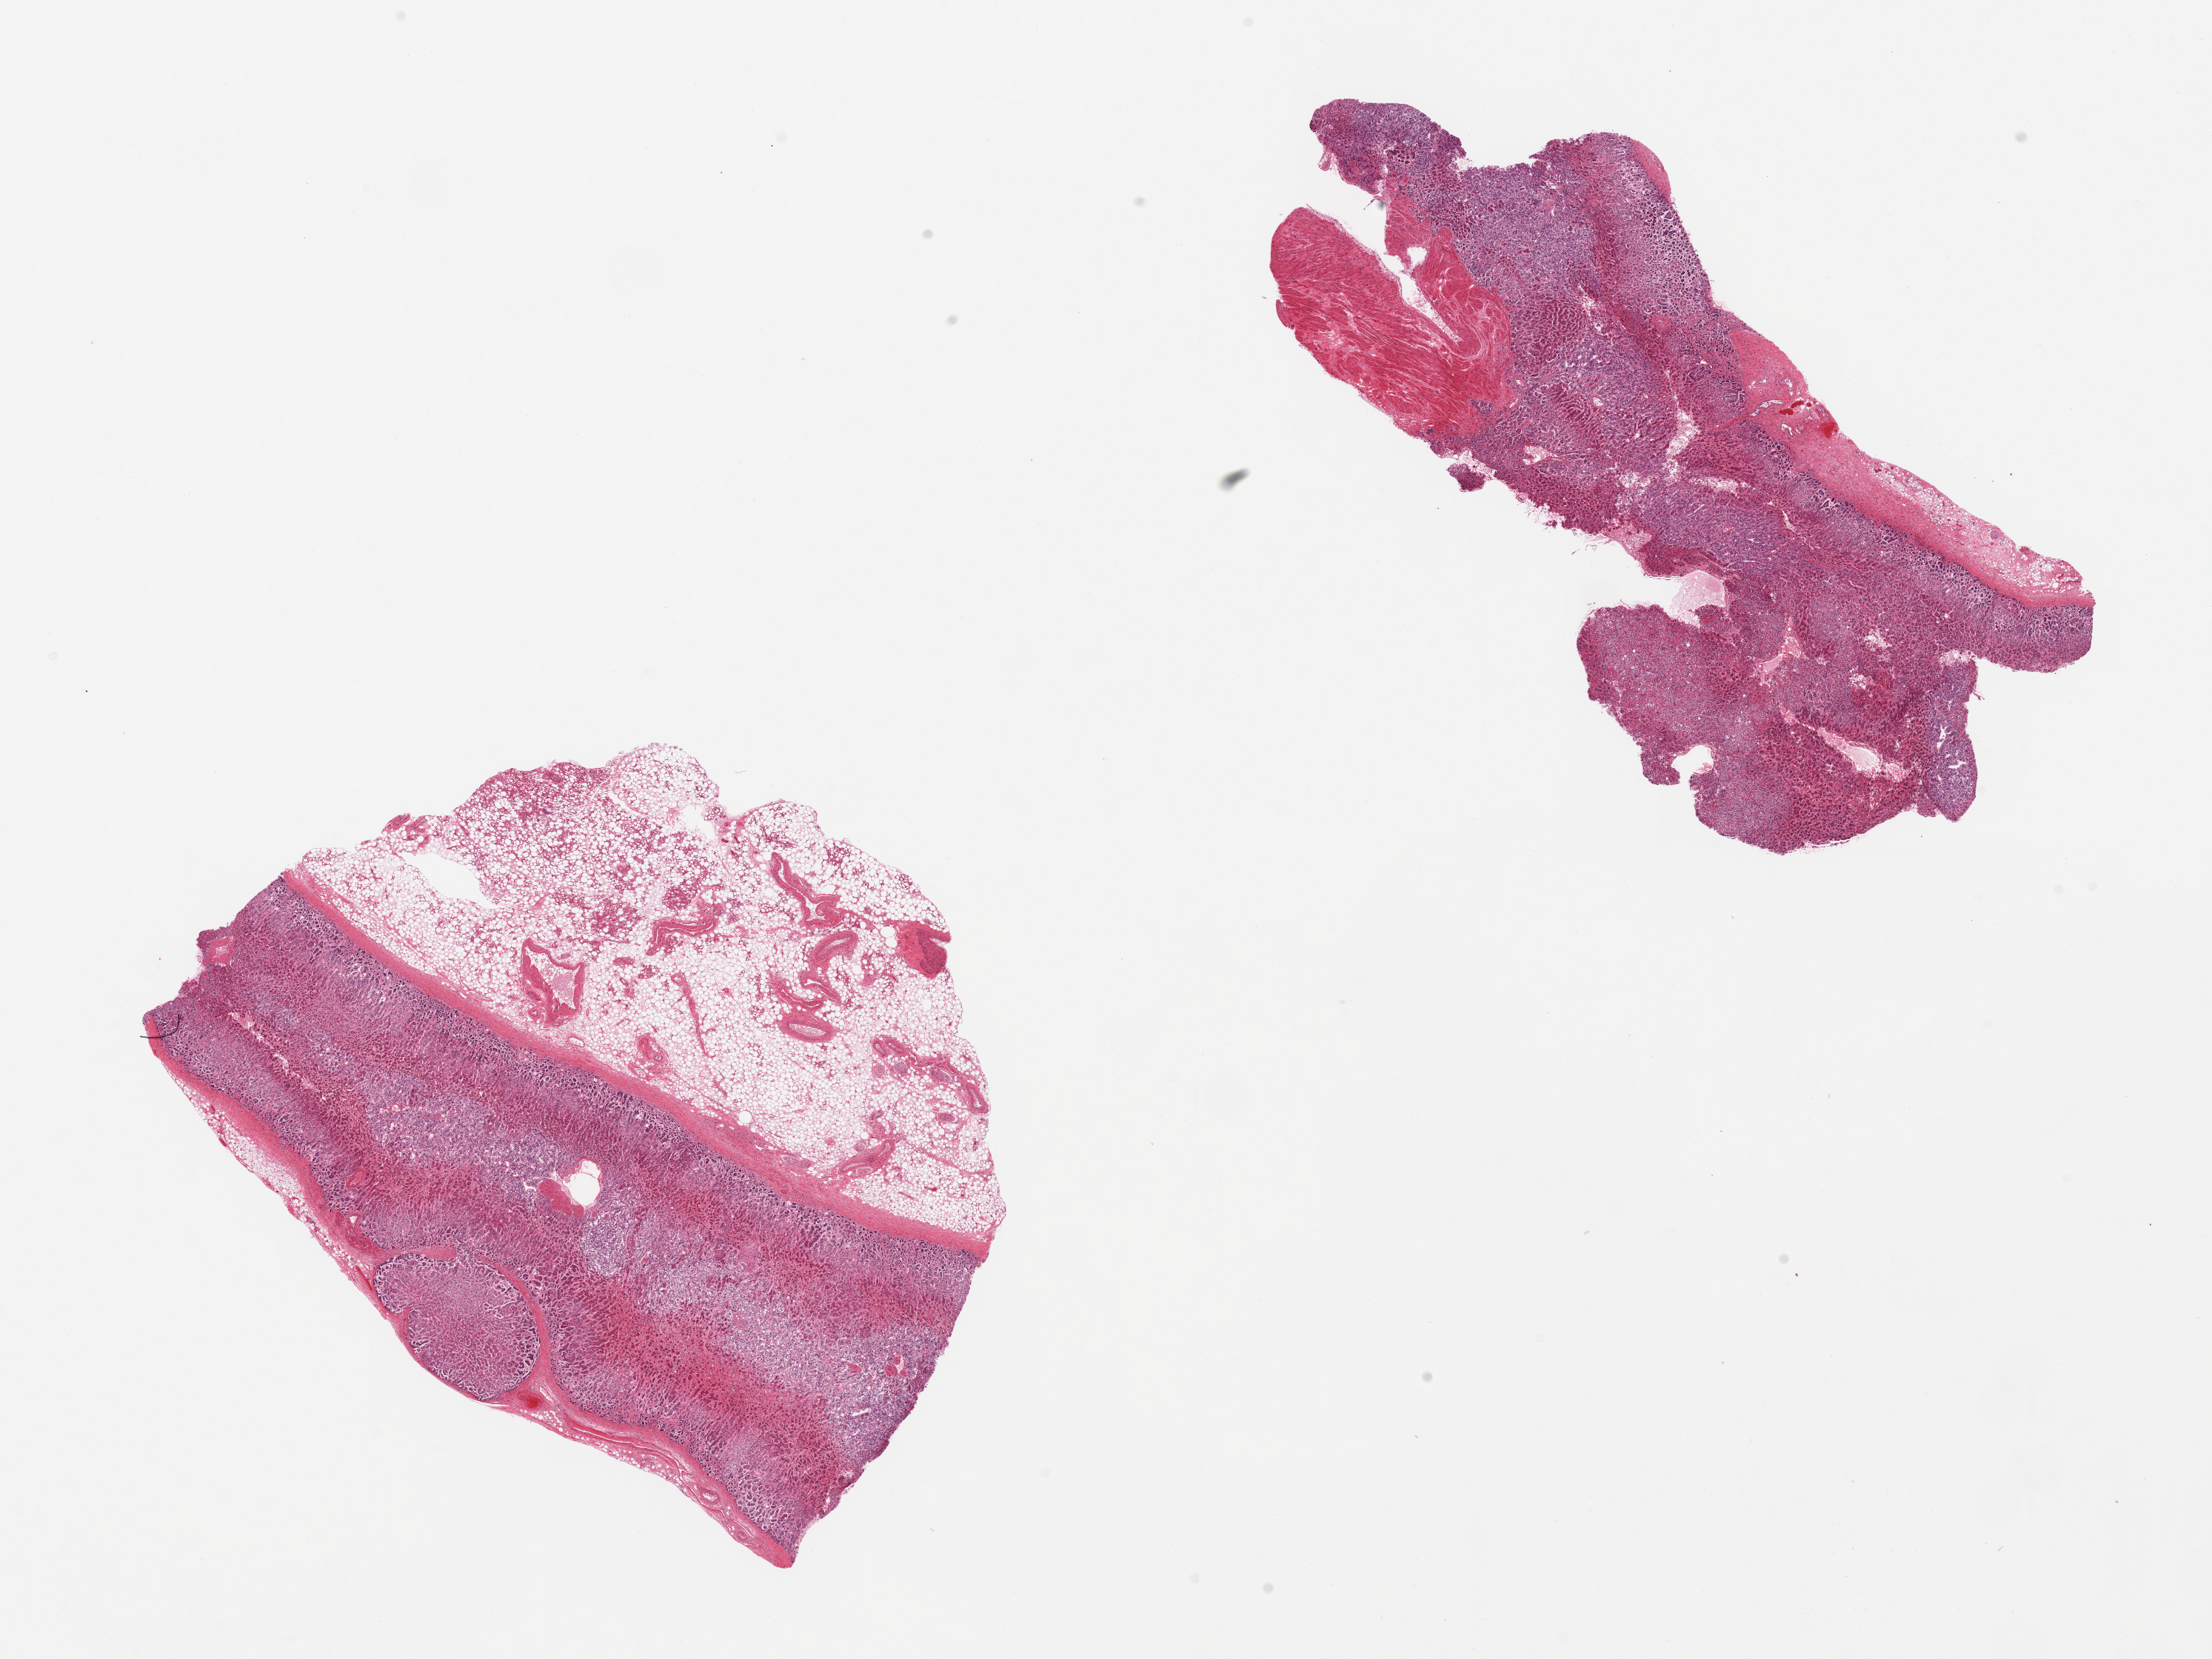
Hematoxylin and eosin (H&E) whole-slide image, a low-resolution overview of the entire scanned area, about 23.6 x 17.7 mm (acquisition: 20x scan). PAXgene-fixed, paraffin-embedded tissue. Sampled site (target tissue): adrenal gland. Tissue donor sample. Donor sex: female.
Reviewer comment on this tissue sample: 2 pieces; 1 has 50% external fat; other has 30% external stroma.